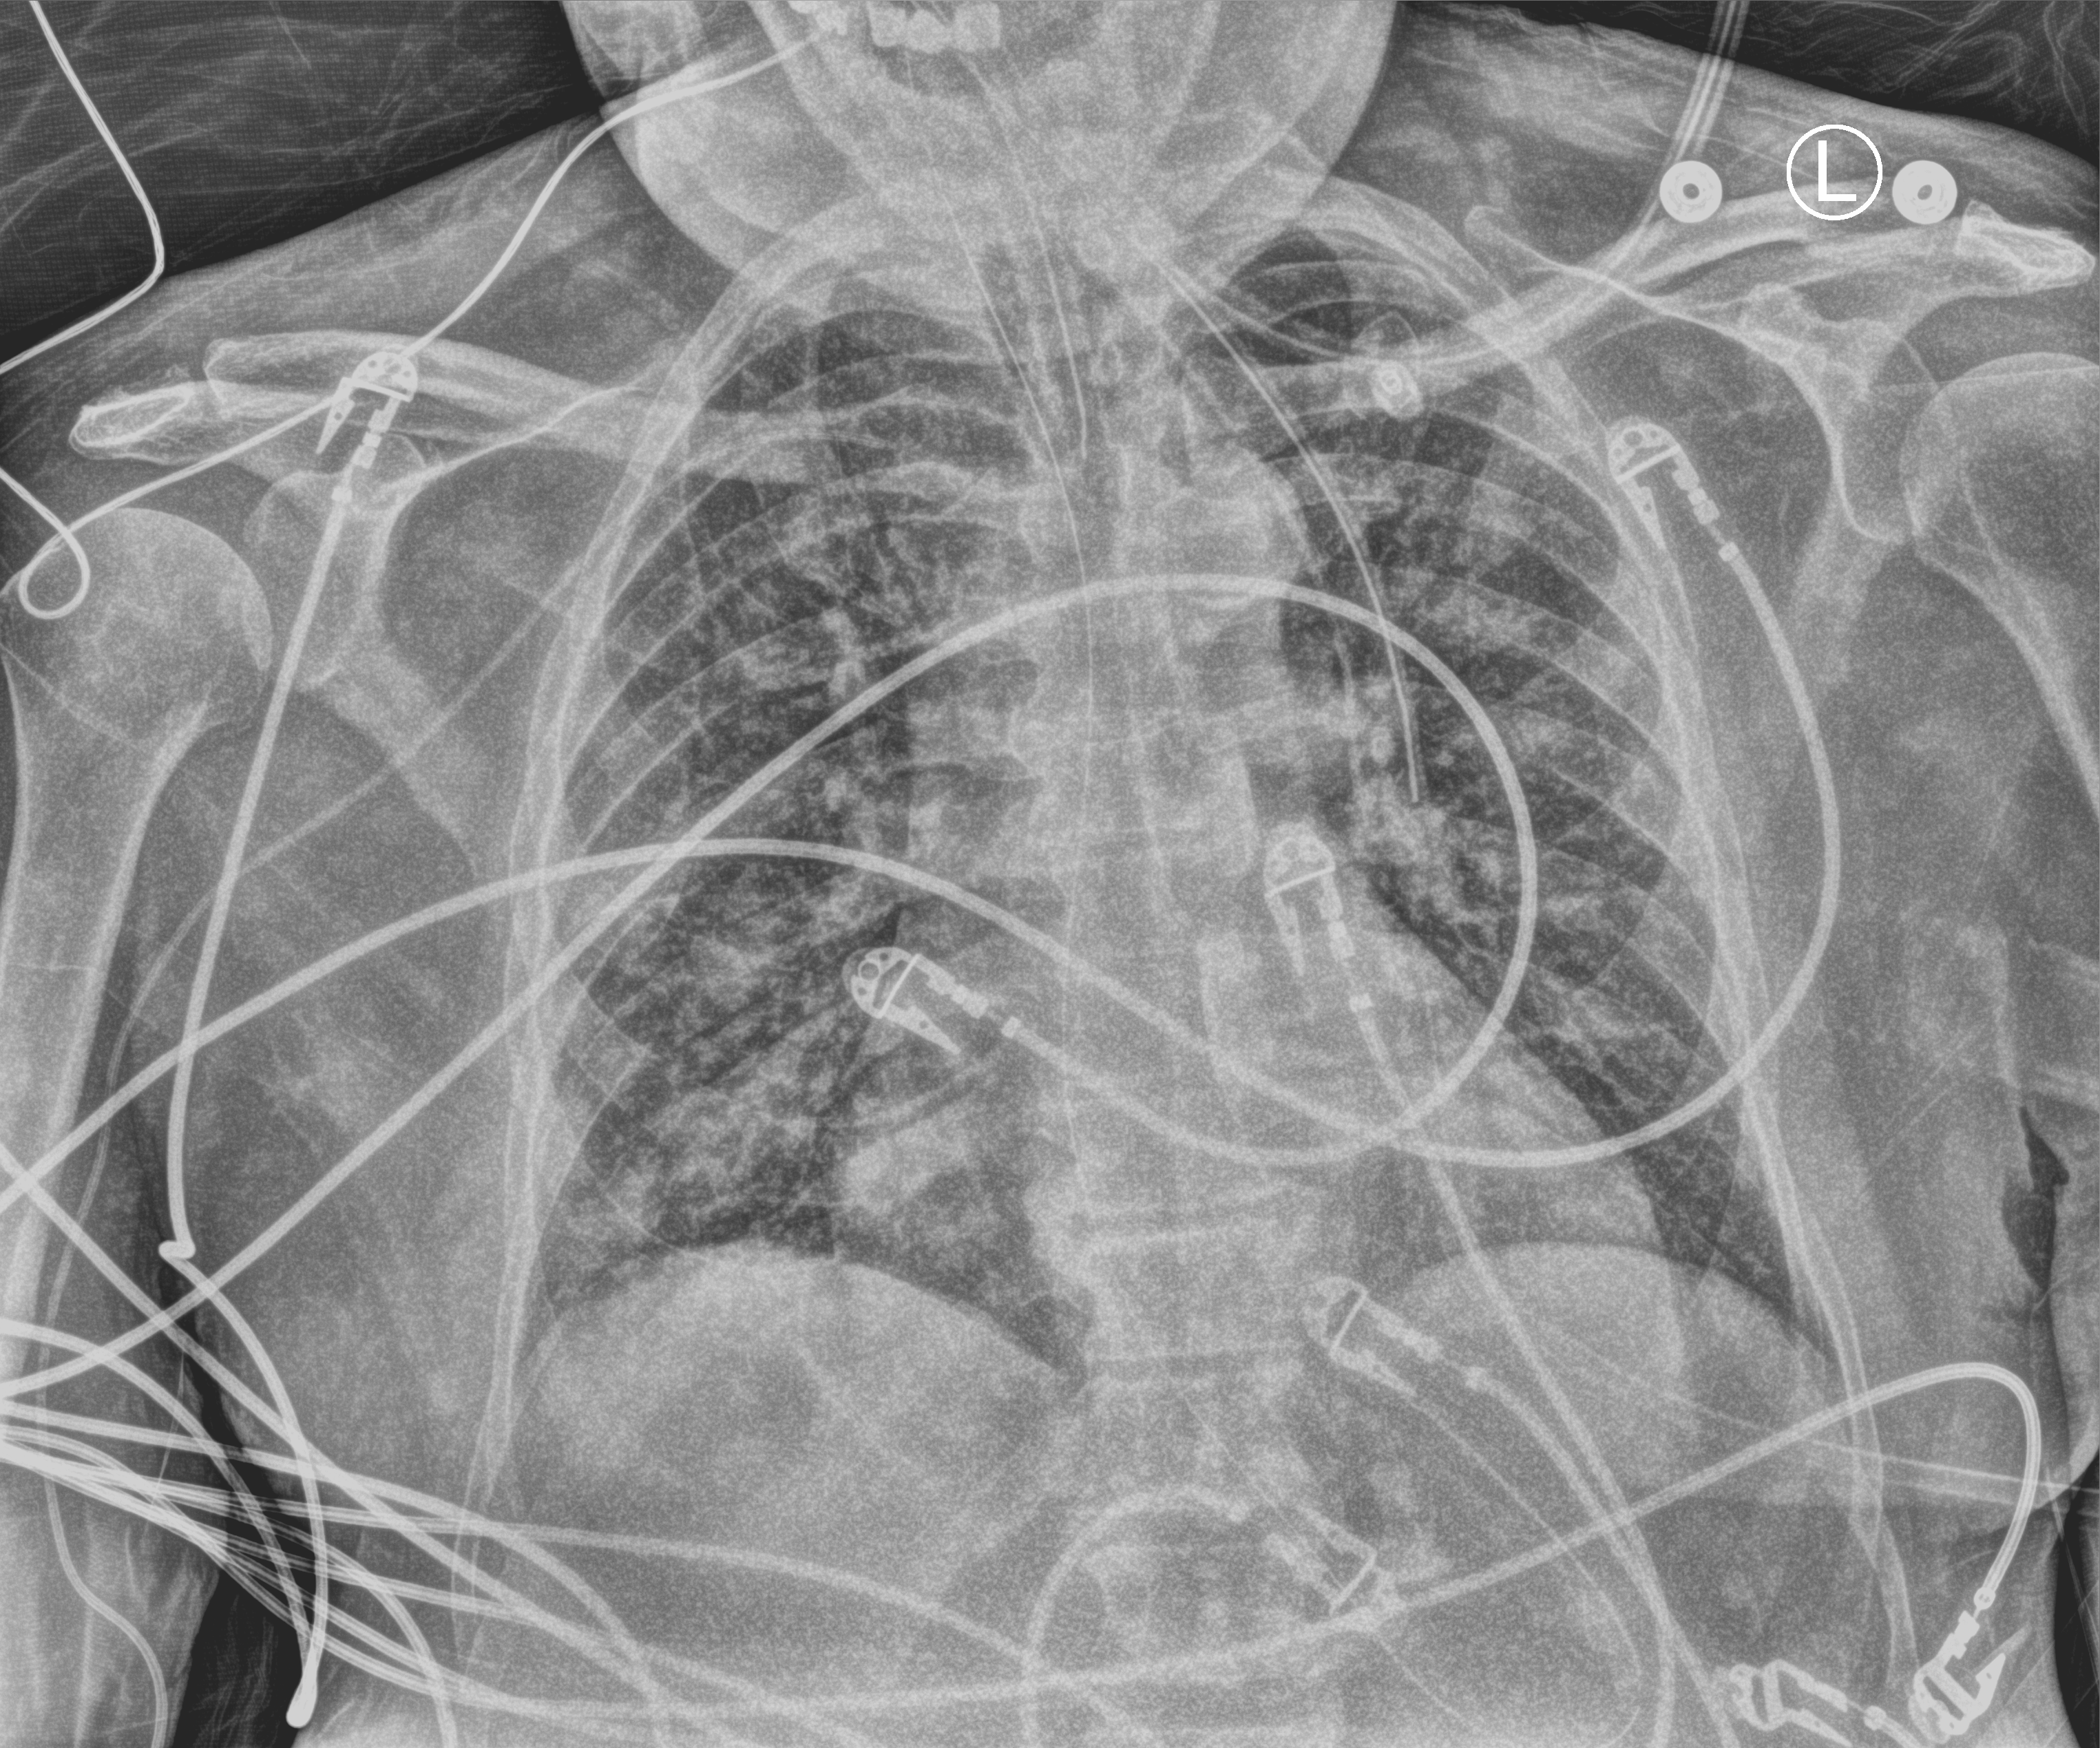
Portable chest radiograph; anteroposterior (AP) projection. Patient hospitalised with COVID-19; male, aged 60–74 years.
Admission-level facts for this patient (not findings on this image; timing relative to this image not recorded): mechanically ventilated during this hospital stay: yes.